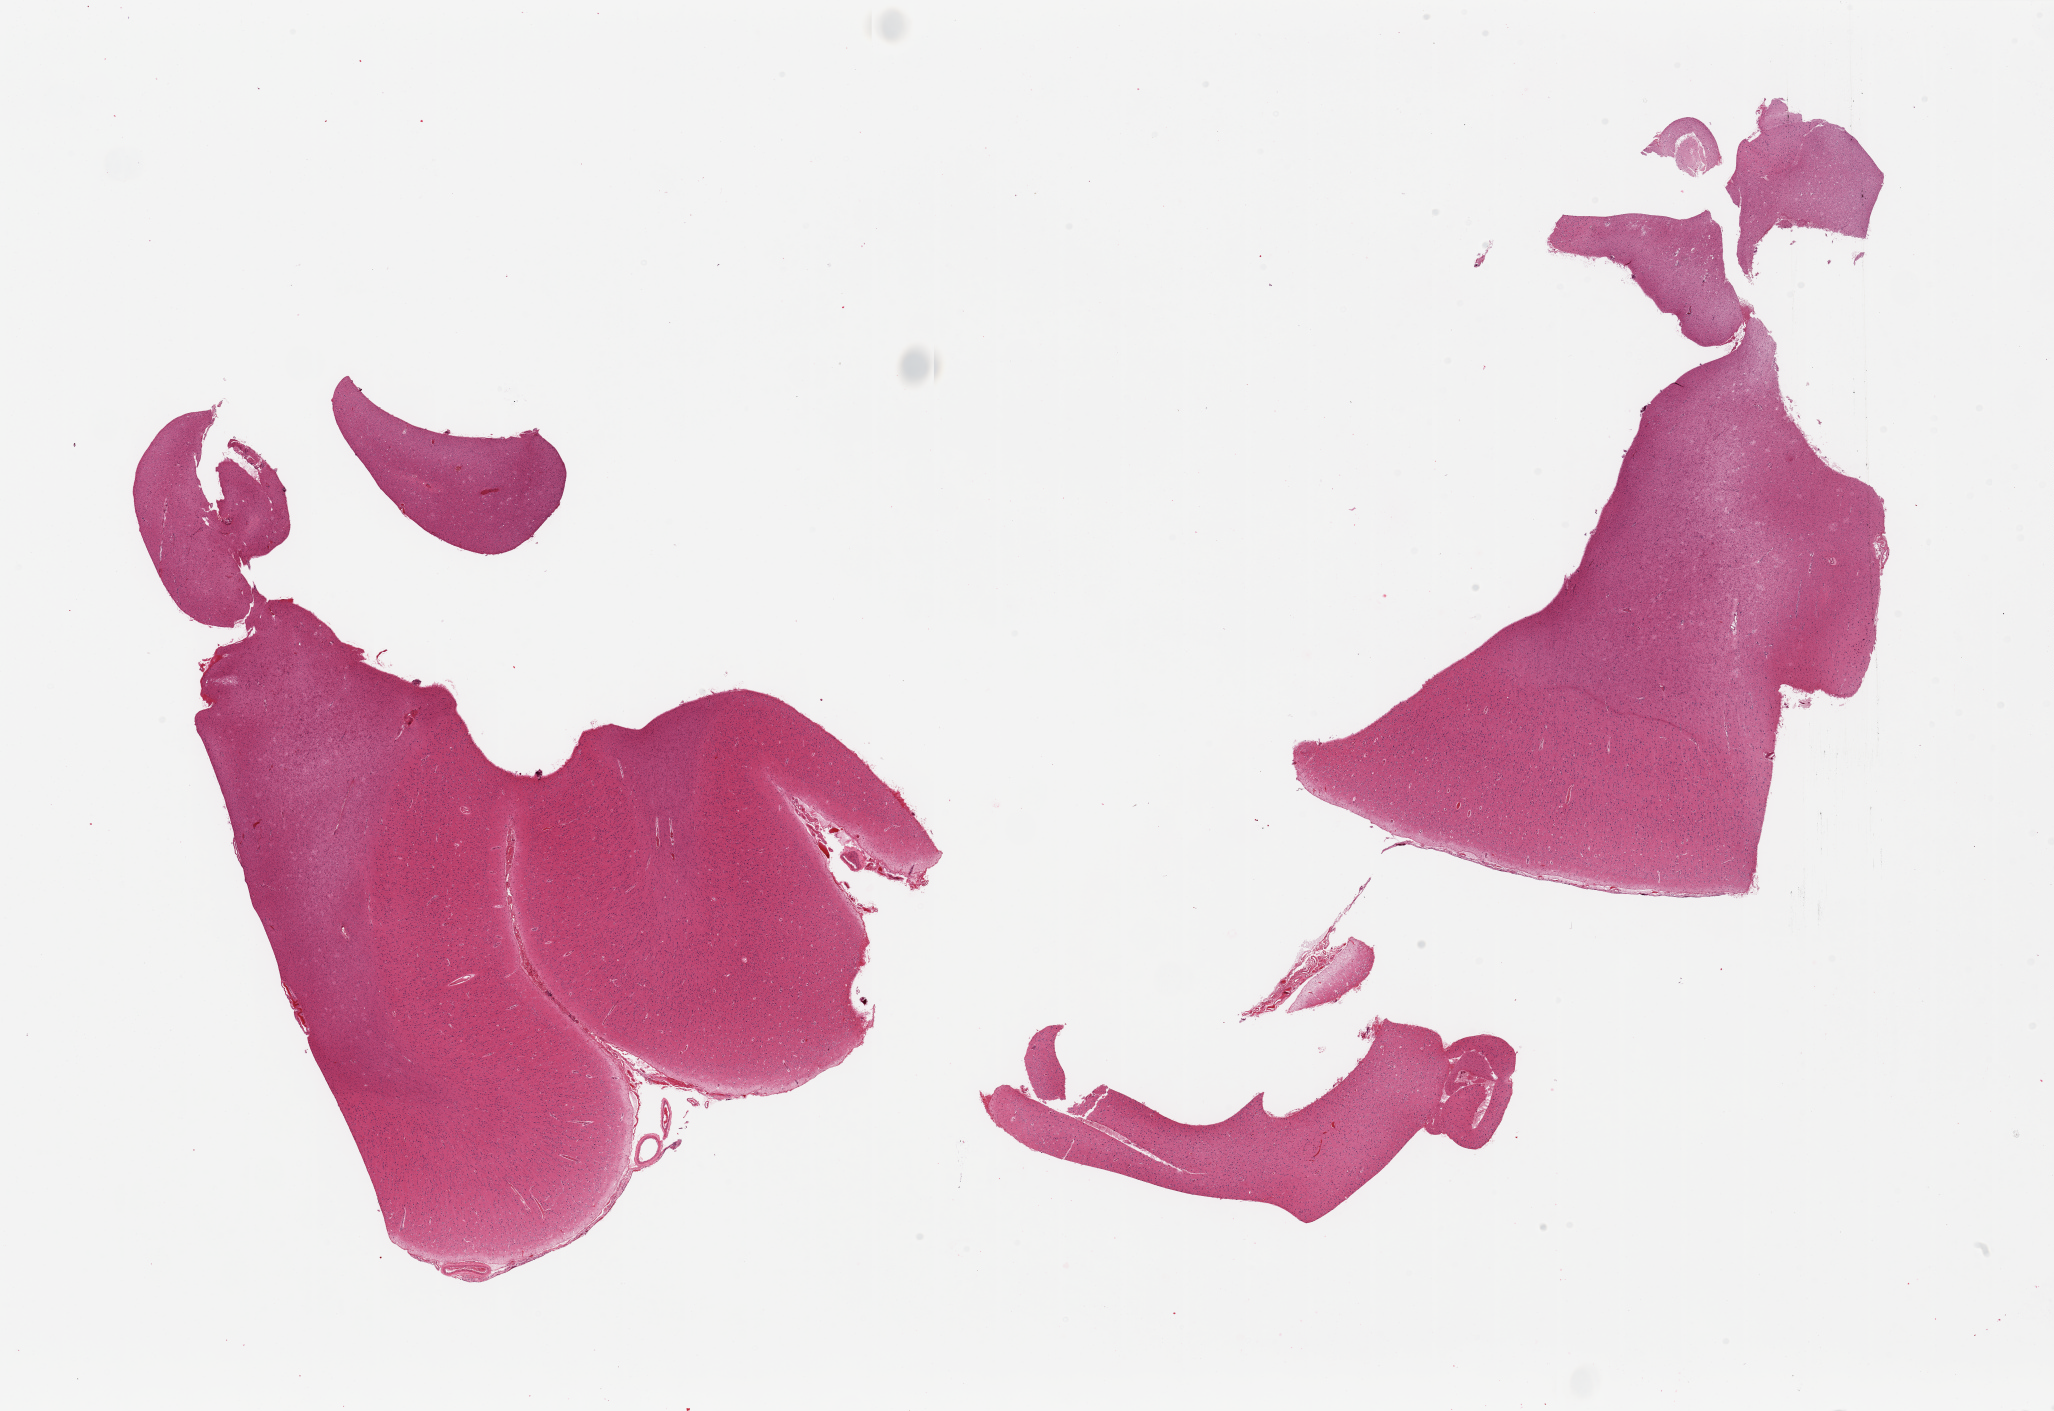
Whole-slide image, H&E stain, brightfield — a low-resolution overview of the entire scanned area, about 32.5 x 22.3 mm; PAXgene-fixed paraffin-embedded (PFPE) section; section of cerebral cortex (target tissue); donor tissue sample. Male donor.
• review note (as recorded): 3 pieces; some attached meninges